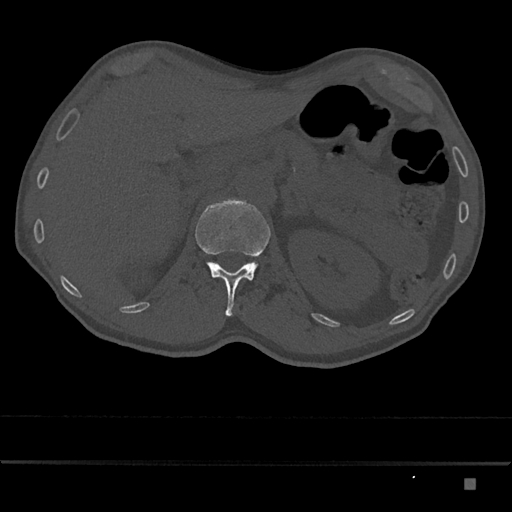
CT including the spine, one axial slice; slice 541 of 797 in the series (ordered by position); reconstruction kernel Br40s/3; 120 kVp; bone window (W 1800 / L 400 HU); 512 × 512 image matrix, field of view 390 × 390 mm. Patient: male, 72 years. Case-level facts recorded for this patient, not image findings: primary cancer: prostate.
Structures marked on this image (semi-automatically segmented with operator editing):
- L1 vertebra: bounding box (x1, y1, x2, y2) in pixels: (195, 198, 271, 317)